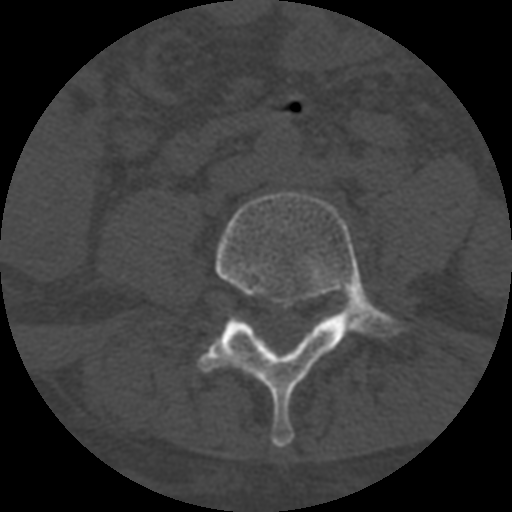
CT including the spine, one axial slice; slice 205 of 708 in the series (ordered by position); one of 3 acquisitions stored at this slice position; bone window (W 1800 / L 400 HU); 1.25 mm slice thickness; 512 × 512 image matrix, field of view 160 × 160 mm. Patient age 55 years. From the clinical record (not read from this slice): primary cancer: colon; vertebrae with lytic lesions (as recorded): T12, L1, L5.
Annotated regions visible in this slice (semi-automatic segmentation, software-assisted and operator-edited):
- L4 vertebra: box from (x=198, y=191) to (x=400, y=448) px
- L5 vertebra: (x=321, y=314)–(x=337, y=322)